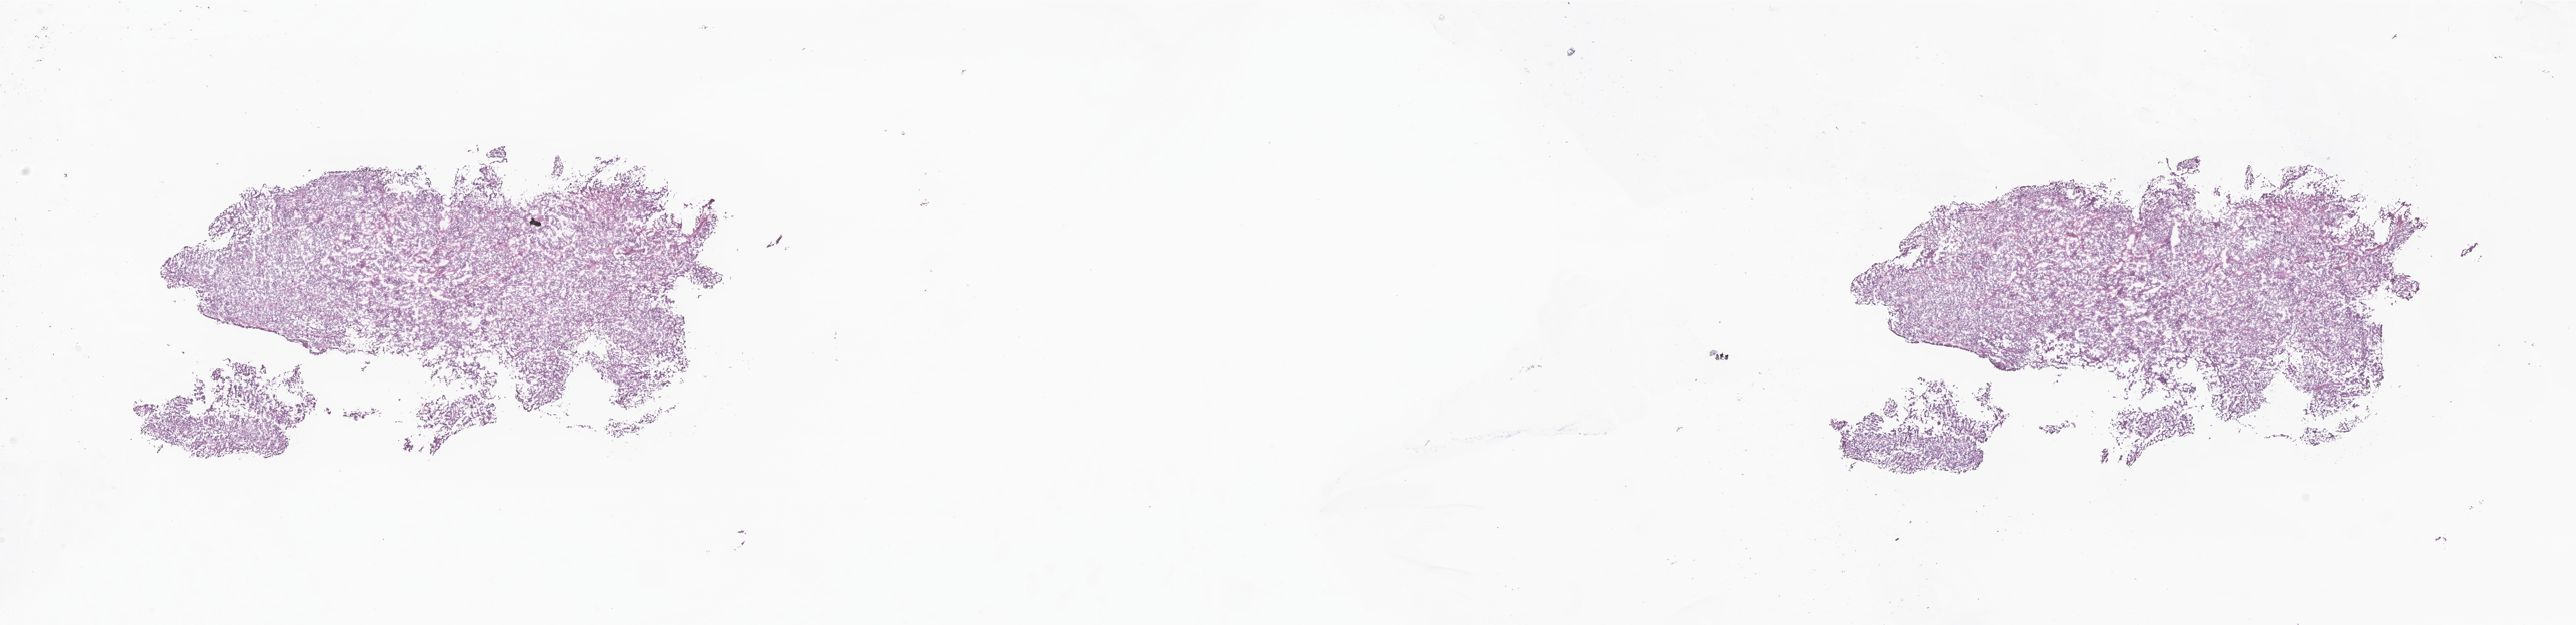
Whole-slide image, hematoxylin and eosin (H&E) stain of tumor tissue from the brain, low-resolution overview of the scanned area, about 33.8 x 8.2 mm. Cryosection (OCT / tissue freezing medium). Patient: male, age 177 months.
Diagnosis (ICD-O-3 morphology term): Ependymoma, NOS.